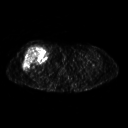
FDG PET of an extremity soft-tissue mass (from a PET/CT study), one axial slice. Slice 264 of 311 in the series (ordered by position). 128 × 128 image matrix, field of view 500 × 500 mm. Female patient, age 57 years. Case-level facts recorded for this patient, not image findings: histological type: pleiomorphic undifferentiated sarcoma; grade: high; site of the primary tumour: right quadricep.
Annotated regions visible in this slice (expert contour drawn on MRI and transferred to this co-registered scan by the dataset authors):
- tumour plus oedema (research contour): bounding box (x1, y1, x2, y2) in pixels: (22, 46, 48, 70)
- tumour (research contour): (22, 46, 48, 70)